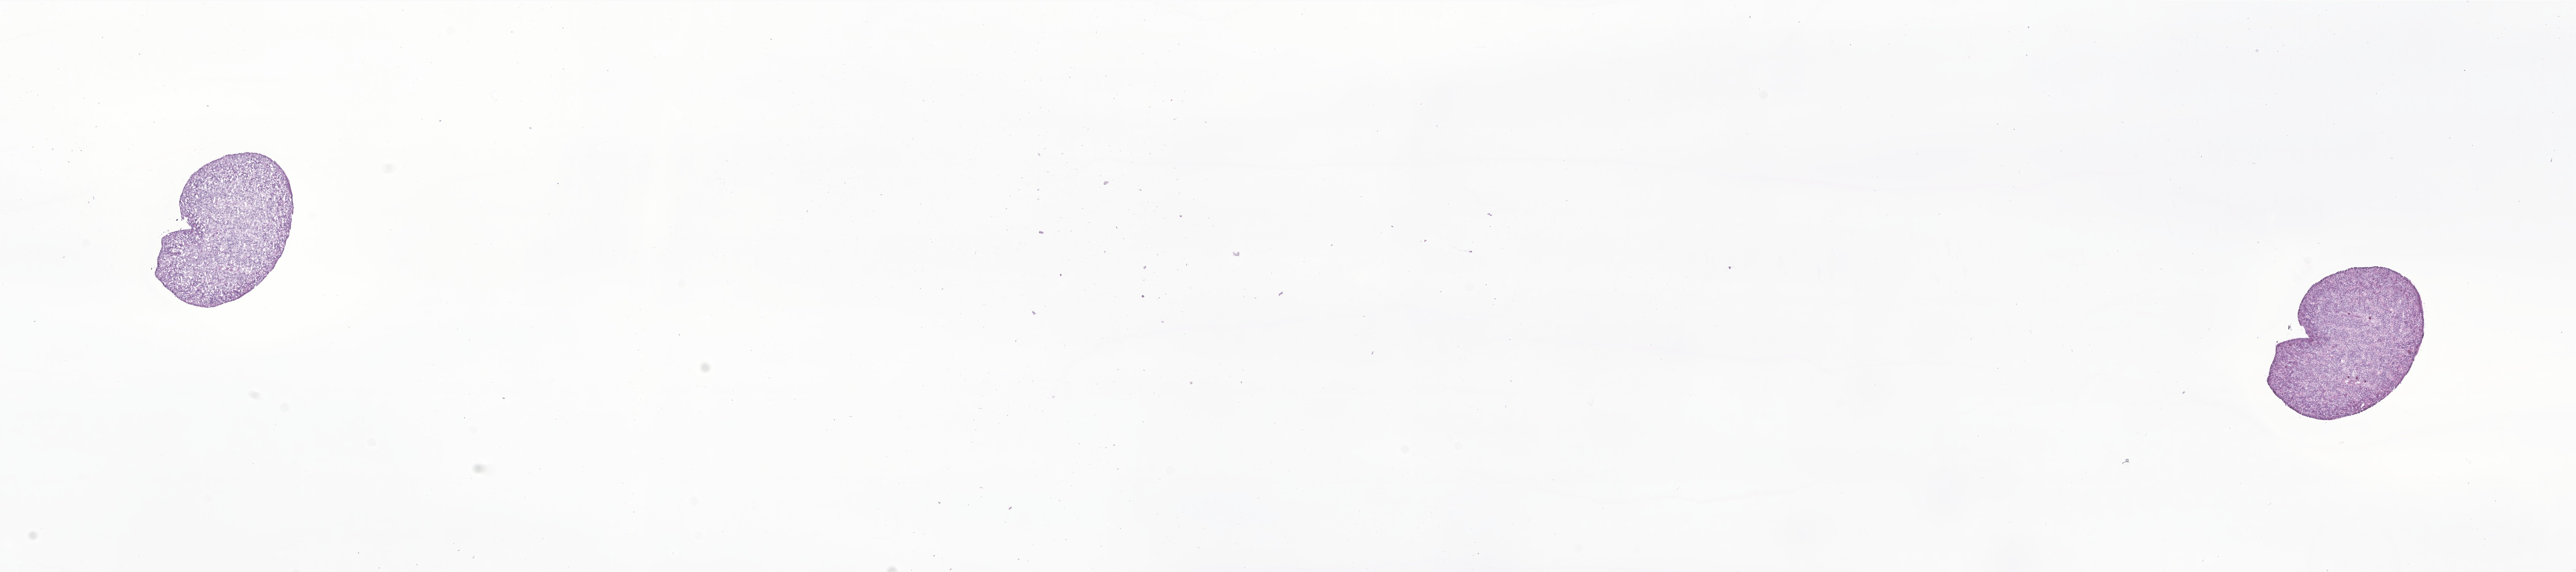
Whole-slide image, hematoxylin and eosin (H&E) stain of tumor tissue from the brain, a low-resolution overview of the entire scanned area, about 30.9 x 6.9 mm; cryosection (OCT / tissue freezing medium). Patient: male, age 131 days.
Diagnosis: Neoplasm, uncertain whether benign or malignant.